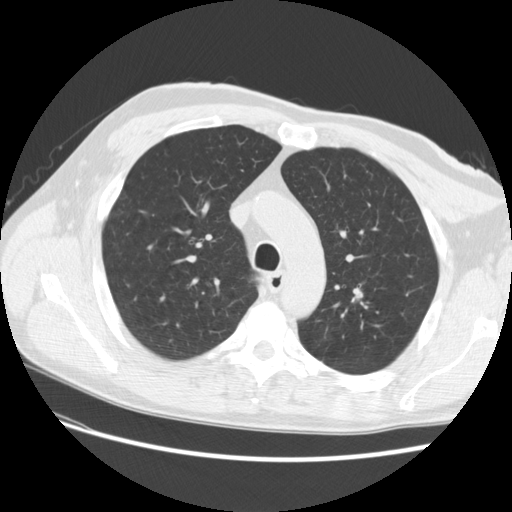
Low-dose screening chest CT, one axial slice. Position 189 of 256 along the scan axis. Reconstruction kernel STANDARD. 120 kVp. Lung window (W 1500 / L -600 HU). 512 × 512 image matrix, field of view 366 × 366 mm.
Outlined on this slice (outlined manually by an expert reader):
- lesion 1 (tumor, upper lobe of left lung): bounding box <355,293,362,298> (left, top, right, bottom; pixels)